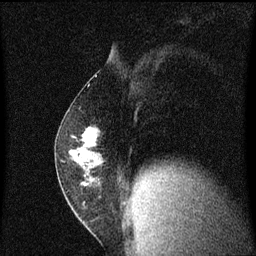
Breast MRI (dynamic contrast-enhanced), one sagittal slice; position 31 of 60 along the scan axis; dynamic contrast-enhanced series, image 2 of 3 at this slice position (ordered by acquisition); 1.5 T; TE 4.2 ms, TR 8.4 ms; 2 mm slice thickness; 256 × 256 image matrix. Female patient, age 52 years. From the clinical record (not read from this slice): setting: breast cancer imaged before/during neoadjuvant chemotherapy; receptor status: HER2-positive.
Outlined on this slice (semi-automatic segmentation, software-assisted and operator-edited):
- analysis volume of interest (the breast-tissue region the enhancement analysis was run in; not a lesion): bounding box <56,124,106,191> (left, top, right, bottom; pixels)
- tumour enhancement mask (voxels above the 70 % enhancement threshold inside the analysis volume of interest): <70,128,97,185>